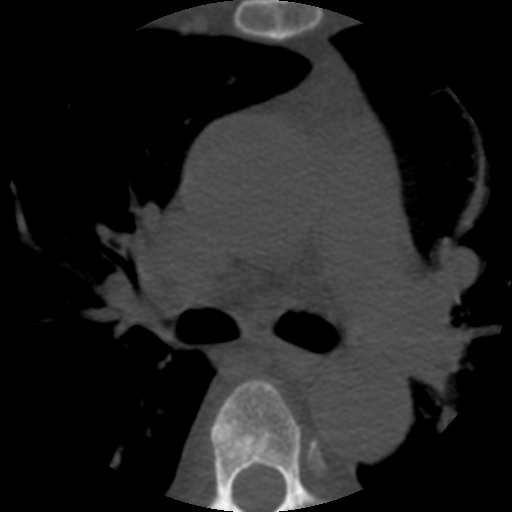
CT including the spine, one axial slice. Slice 377 of 508 in the series (ordered by position). 120 kVp. Bone window (W 1800 / L 400 HU). 1.25 mm slice thickness. 512 × 512 image matrix. Patient age 57 years. Case-level facts recorded for this patient, not image findings: primary cancer: prostate.
Annotated regions visible in this slice (semi-automatically segmented with operator editing):
- T5 vertebra: box from (x=211, y=379) to (x=320, y=512) px